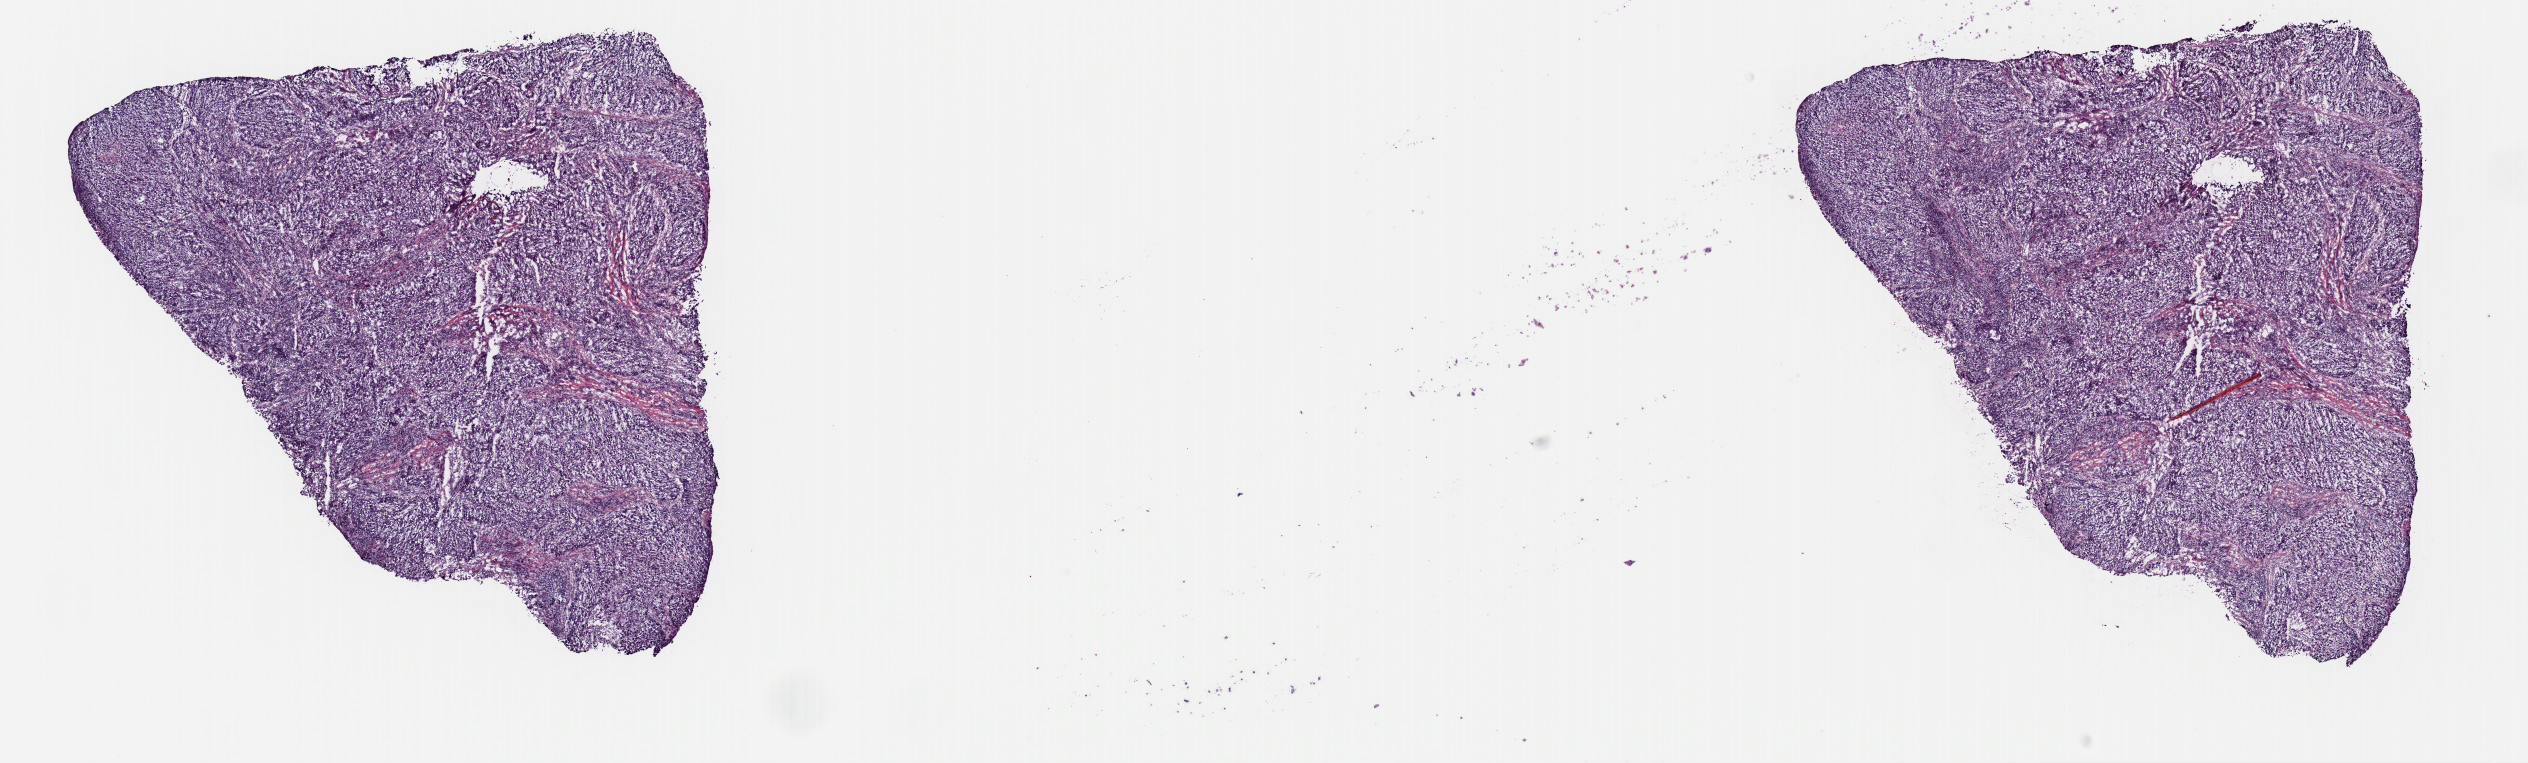
Whole-slide histology image, H&E, whole scanned area (about 20.0 x 6.0 mm, acquisition: 40x scan) shown as a low-resolution overview, frozen section from the top of the tissue portion, sample: primary tumour, lung. Male, age 61 years at initial diagnosis. Slide review estimates, as recorded: tumour cells 67%, tumour nuclei 80%, normal cells 0%, stromal cells 25%, necrosis 8%. Infiltration values recorded for this section: lymphocyte infiltration 5%, monocyte infiltration 3%, neutrophil infiltration 2%.
- histologic diagnosis: Squamous cell carcinoma, NOS (lower lobe, lung)
- AJCC pathologic stage: IIB (7th edition)